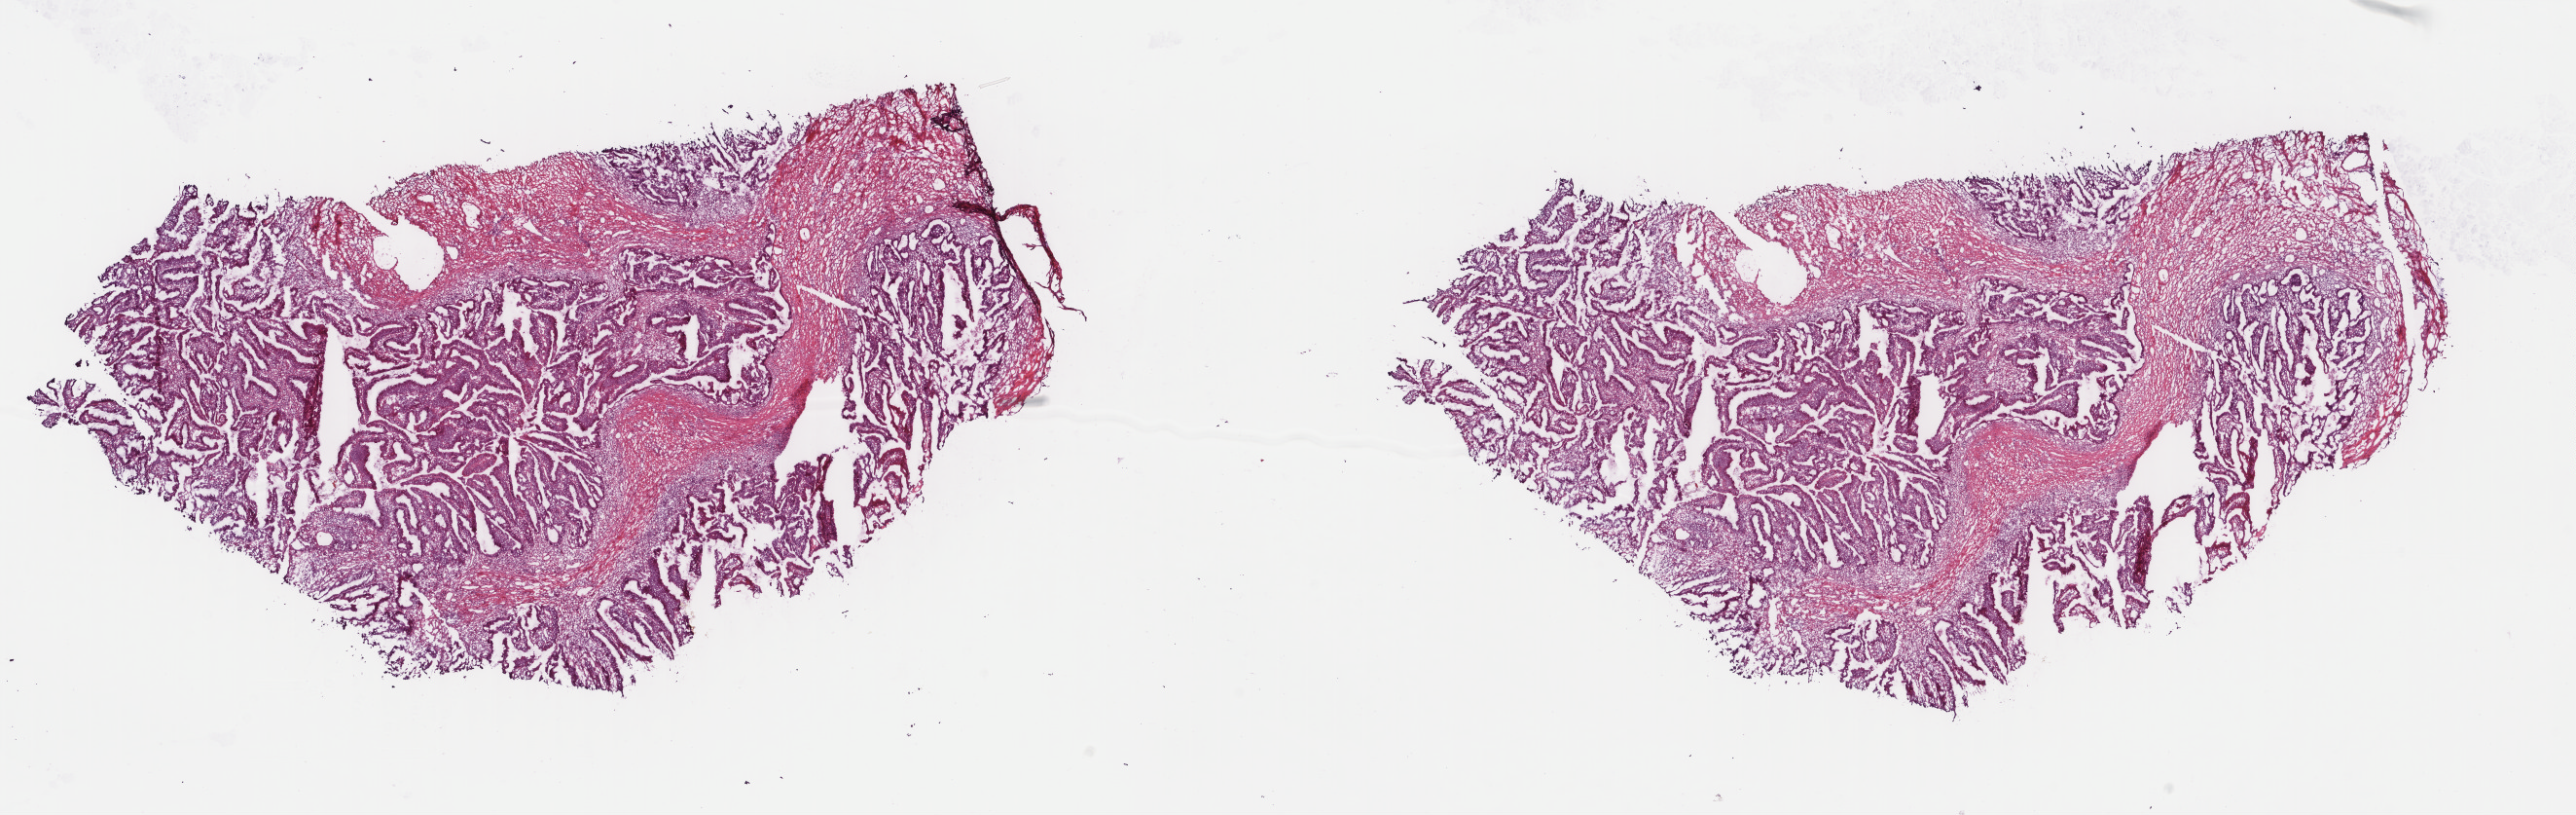
Digitized H&E tissue section (whole slide) — a low-resolution overview of the entire scanned area, about 21.0 x 6.6 mm (acquisition: 40x scan); frozen section from the top of the tissue portion; primary tumour sample from the colon. Male, age 75 years at initial diagnosis. Slide review estimates, as recorded: tumour cells 75%, tumour nuclei 75%, normal cells 0%, stromal cells 23%, necrosis 2%. Inflammatory infiltration, as recorded: lymphocyte infiltration 3%, monocyte infiltration 2%, neutrophil infiltration 2%.
AJCC pathologic stage: IIA (6th edition). Lymph nodes positive (case pathology): 0 of 25 examined. Histologic diagnosis: Adenocarcinoma, NOS (ascending colon).